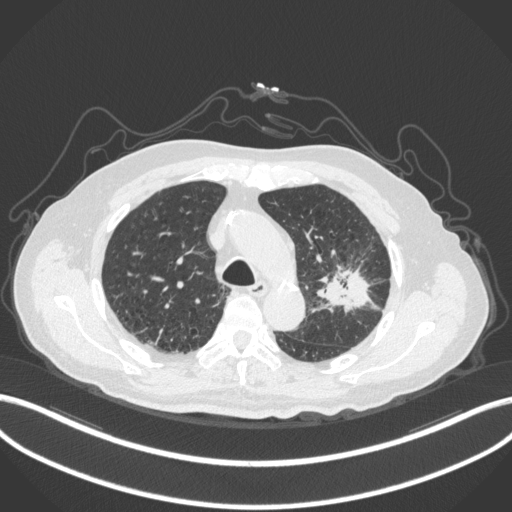
Chest CT, one axial slice. Position 211 of 331 along the scan axis. Lung window (W 1500 / L -600 HU). 1 mm slice thickness. 512 × 512 image matrix, field of view 400 × 400 mm. Male patient, age 79 years. Case-level facts recorded for this patient, not image findings: clinical TNM (as recorded): T2a N1 M1.
Annotated regions visible in this slice (bounding box drawn by a radiologist):
- lung tumour (recorded histology: adenocarcinoma): bounding box (x1, y1, x2, y2) in pixels: (312, 261, 373, 313)